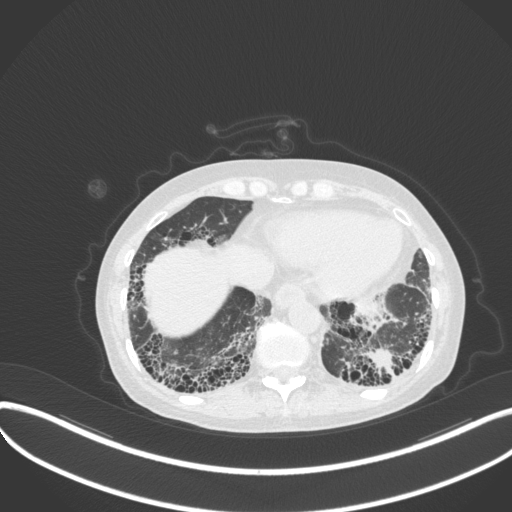
Chest CT, one axial slice; position 67 of 373 along the scan axis; reconstruction kernel B31f; lung window (W 1500 / L -600 HU); 512 × 512 image matrix, field of view 400 × 400 mm. Patient: female, 56 years. From the clinical record (not read from this slice): clinical TNM (as recorded): T1 N0 M0.
Outlined on this slice (rectangle marked by the reading radiologist):
- lung tumour (recorded histology: adenocarcinoma): box from (x=363, y=349) to (x=401, y=379) px